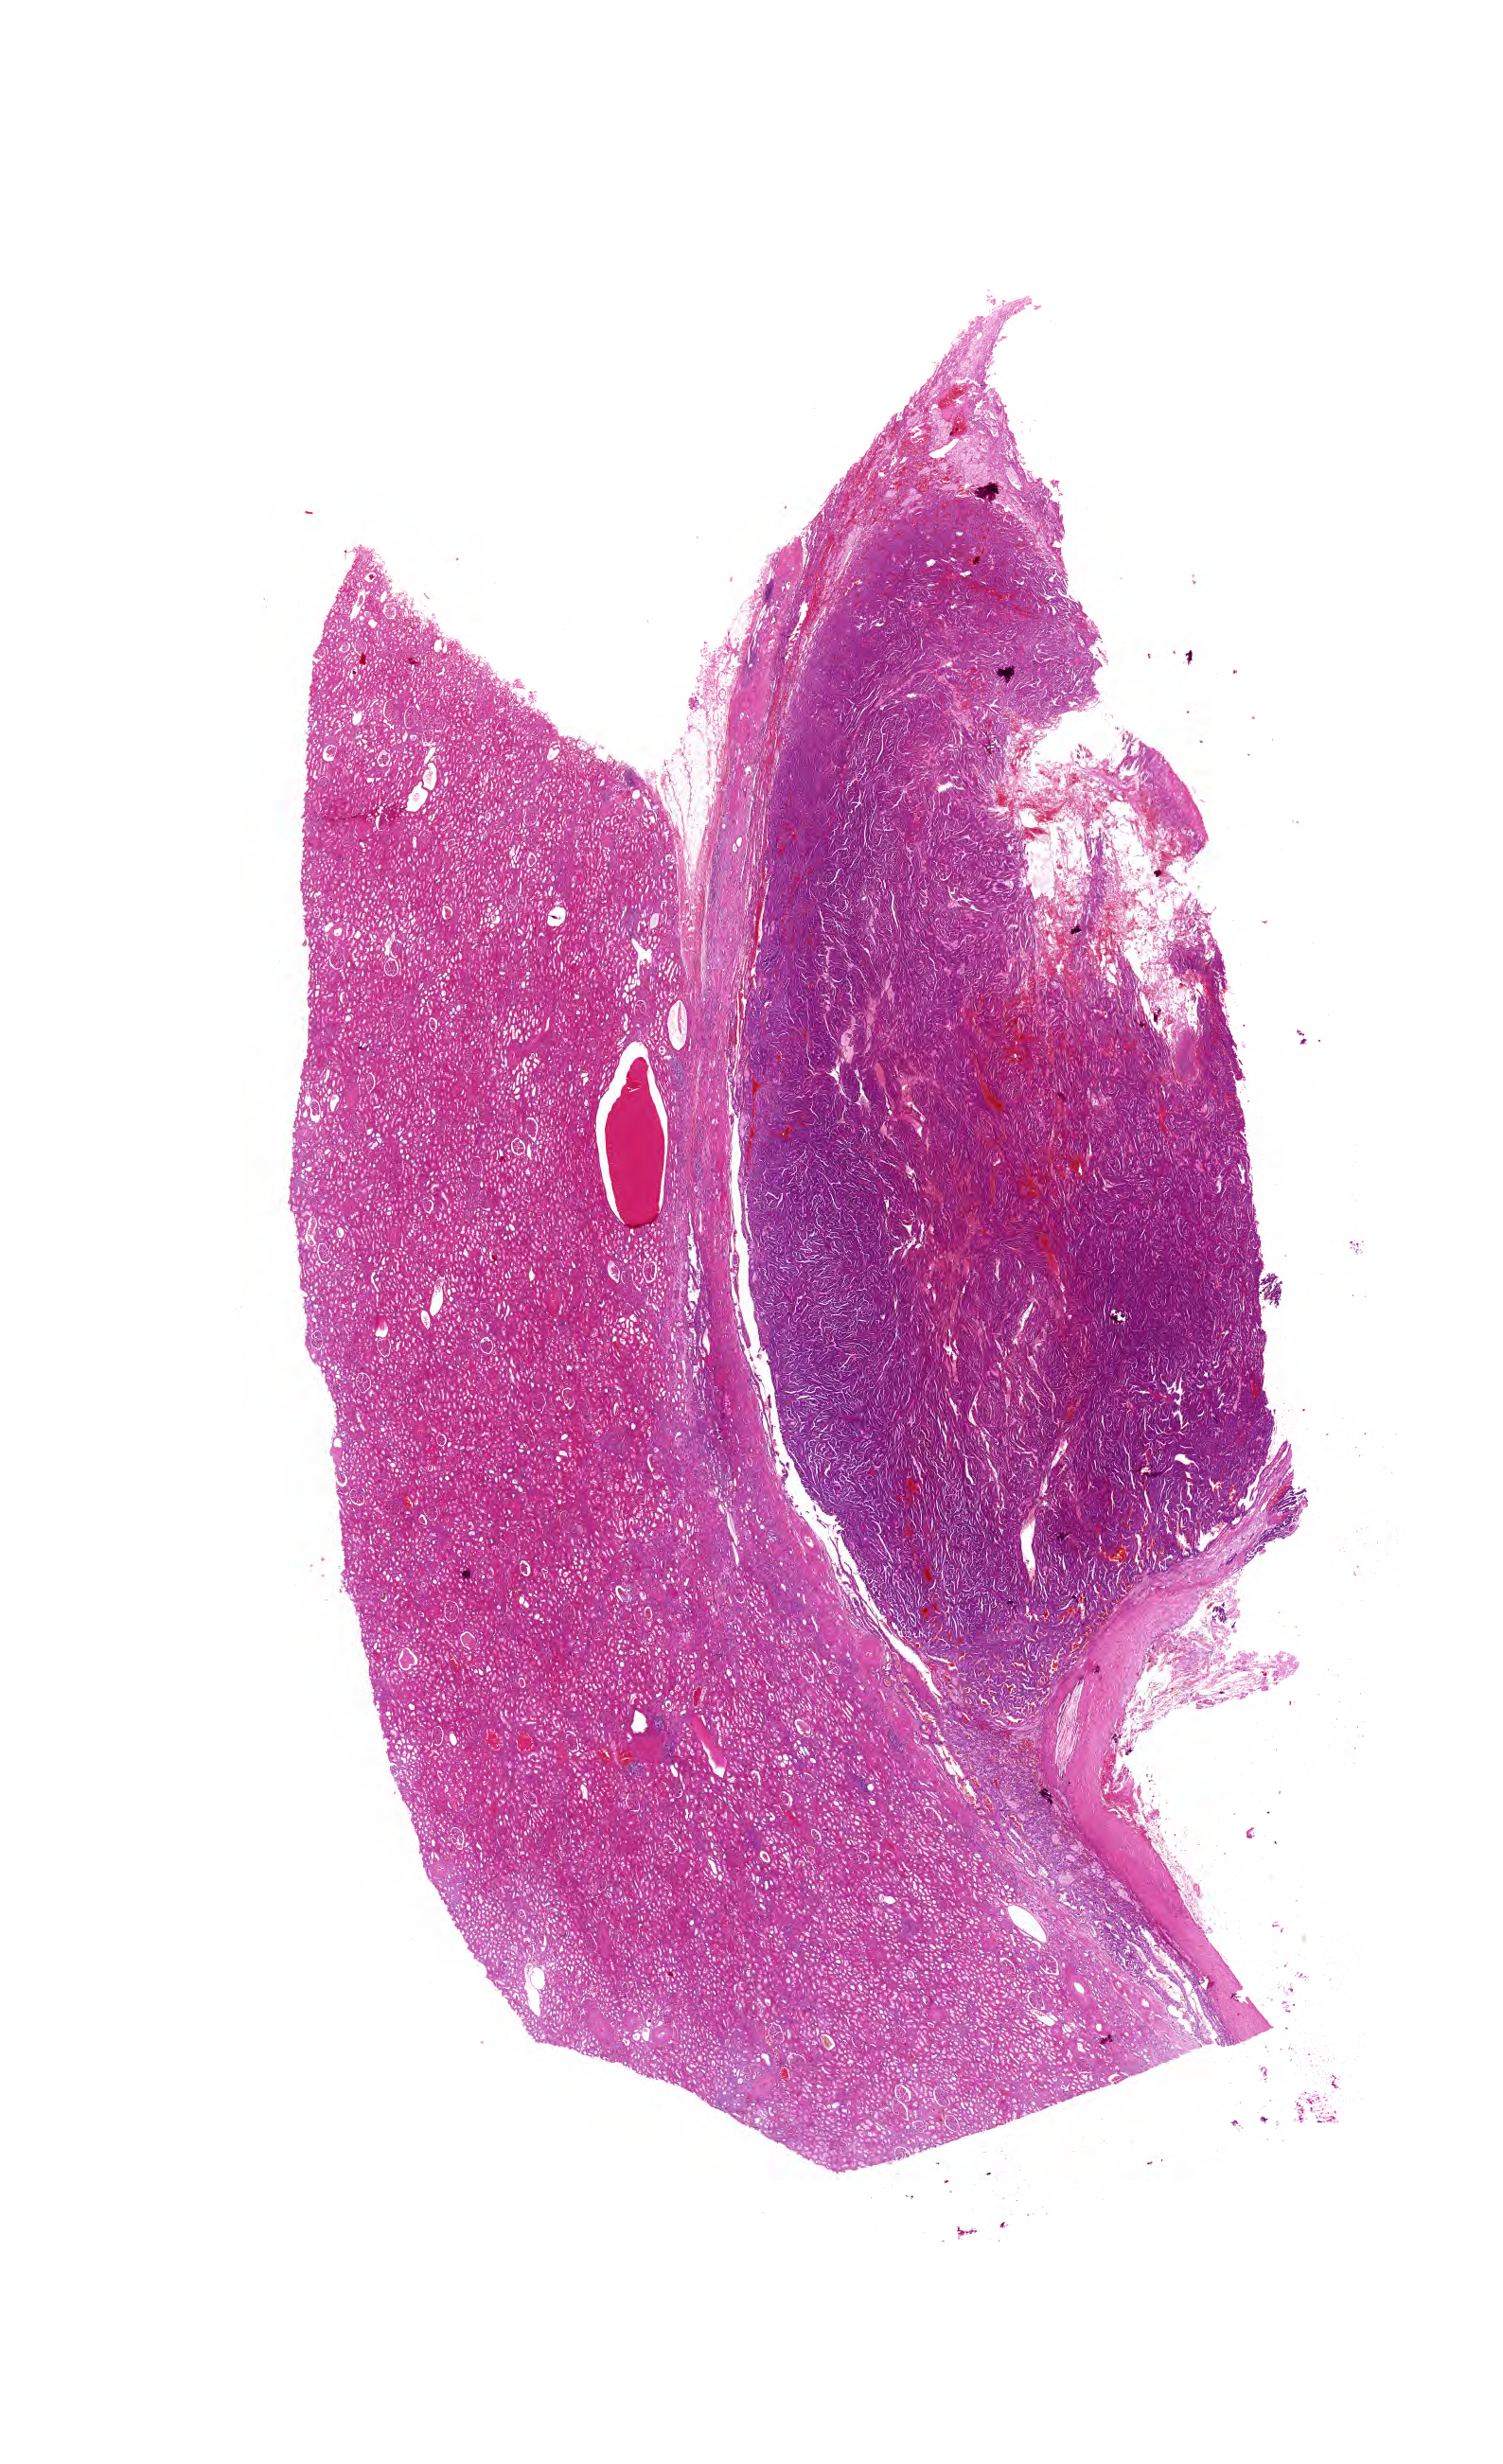
Digitized H&E tissue section (whole slide), low-resolution overview of the scanned area, about 19.8 x 32.4 mm, formalin-fixed paraffin-embedded (FFPE) diagnostic section, sample: primary tumour, kidney. Male, age 79 years at initial diagnosis.
Pathologic diagnosis: Papillary adenocarcinoma, NOS.